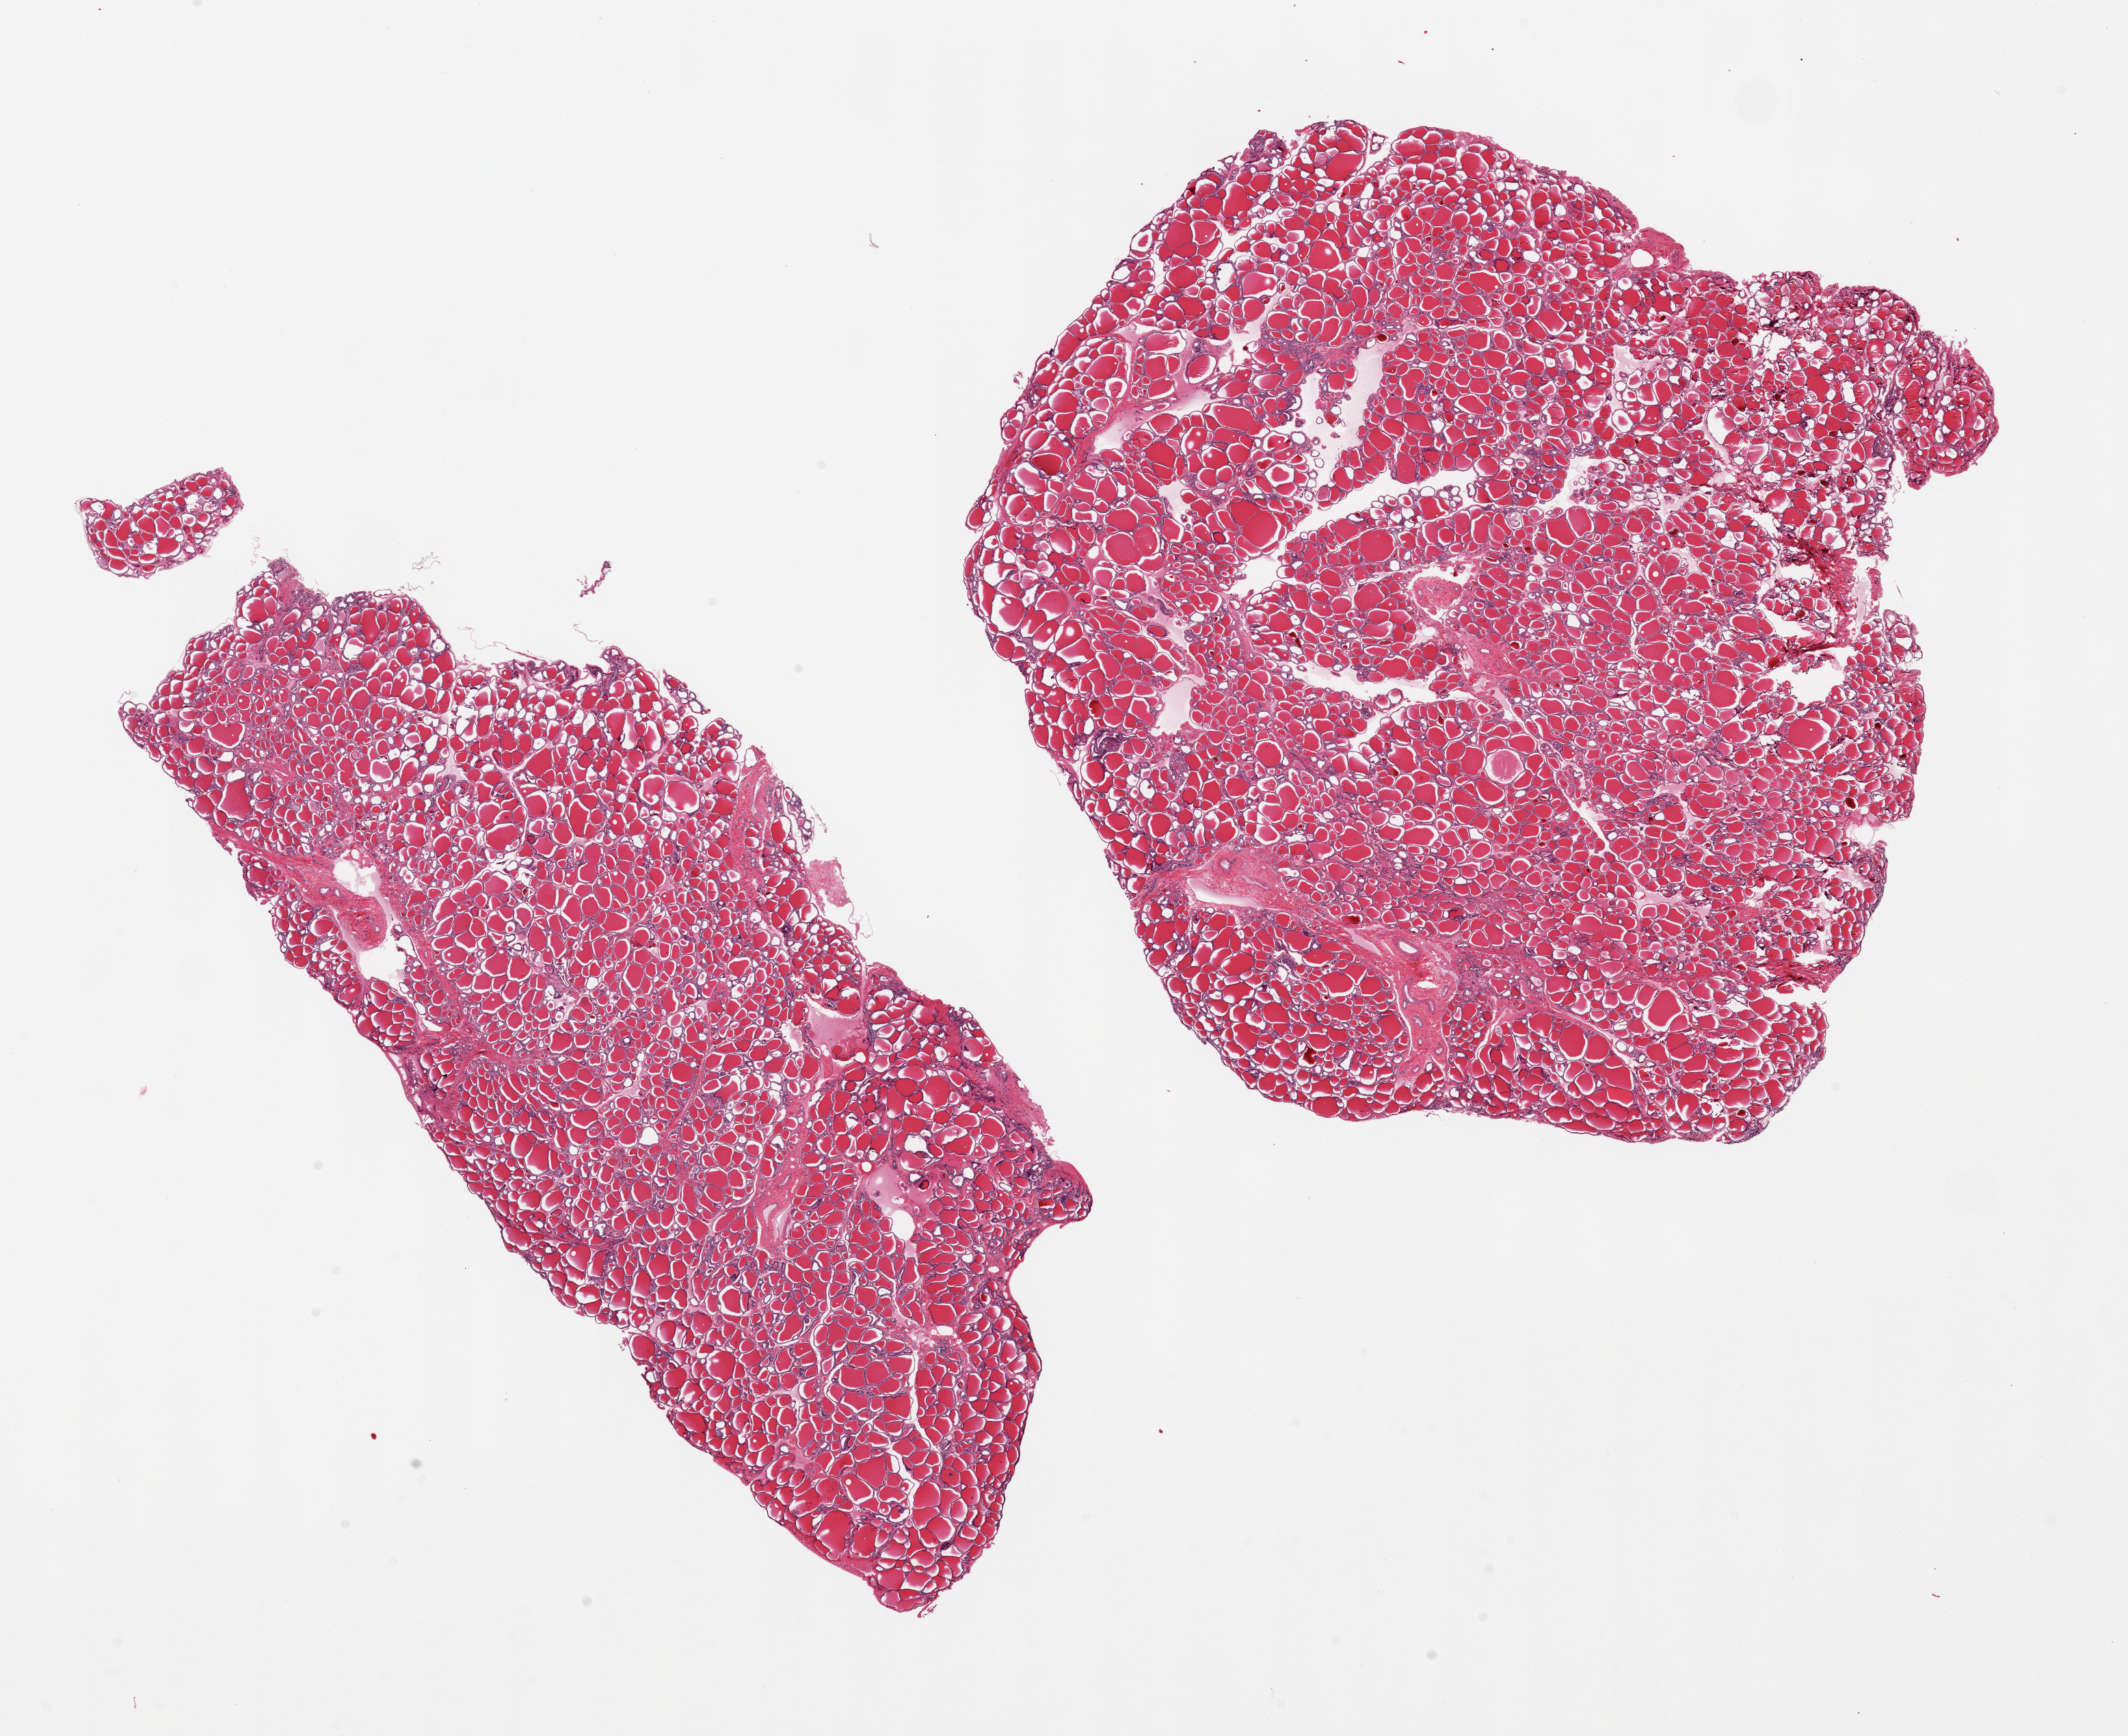
H&E whole-slide image, brightfield, a low-resolution overview of the entire scanned area, about 24.6 x 20.1 mm. PAXgene-fixed paraffin-embedded (PFPE) section. Sampled site (target tissue): thyroid. Donor tissue sample.
• review note (as recorded): 2 pieces. 16x6 & 12x12mm